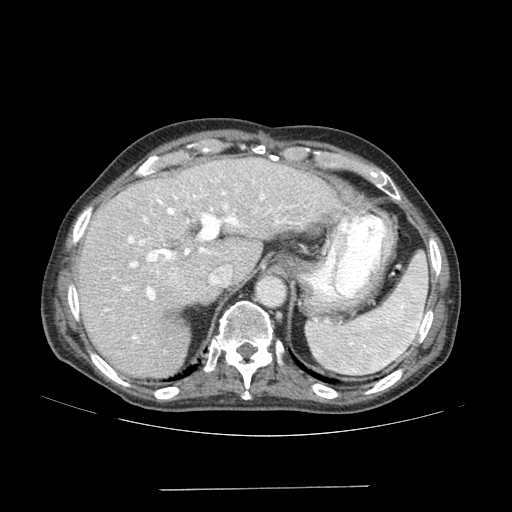
Contrast-enhanced abdominal CT (liver protocol), one axial slice. Slice 116 of 192 in the series (ordered by position). 120 kVp. Soft-tissue window (W 400 / L 40 HU). 2.5 mm slice thickness. 512 × 512 image matrix, field of view 400 × 400 mm. Case-level facts recorded for this patient, not image findings: diagnosis: hepatocellular carcinoma (patient treated with transarterial chemoembolisation; whether this scan precedes or follows treatment is not stated here); TNM stage (as recorded): Stage-IVA; Child-Pugh class: A; tumour differentiation: poorly differentiated; tumour nodularity: uninodular.
Annotated regions visible in this slice (semi-automatic segmentation, software-assisted and operator-edited):
- liver parenchyma outside the tumour (the mass and vessels are separate outlines, so this box may not span the whole liver): bounding box [x1, y1, x2, y2] px = [78, 158, 344, 378]
- mass: [142, 259, 186, 291]
- liver vessels: [105, 180, 291, 343]